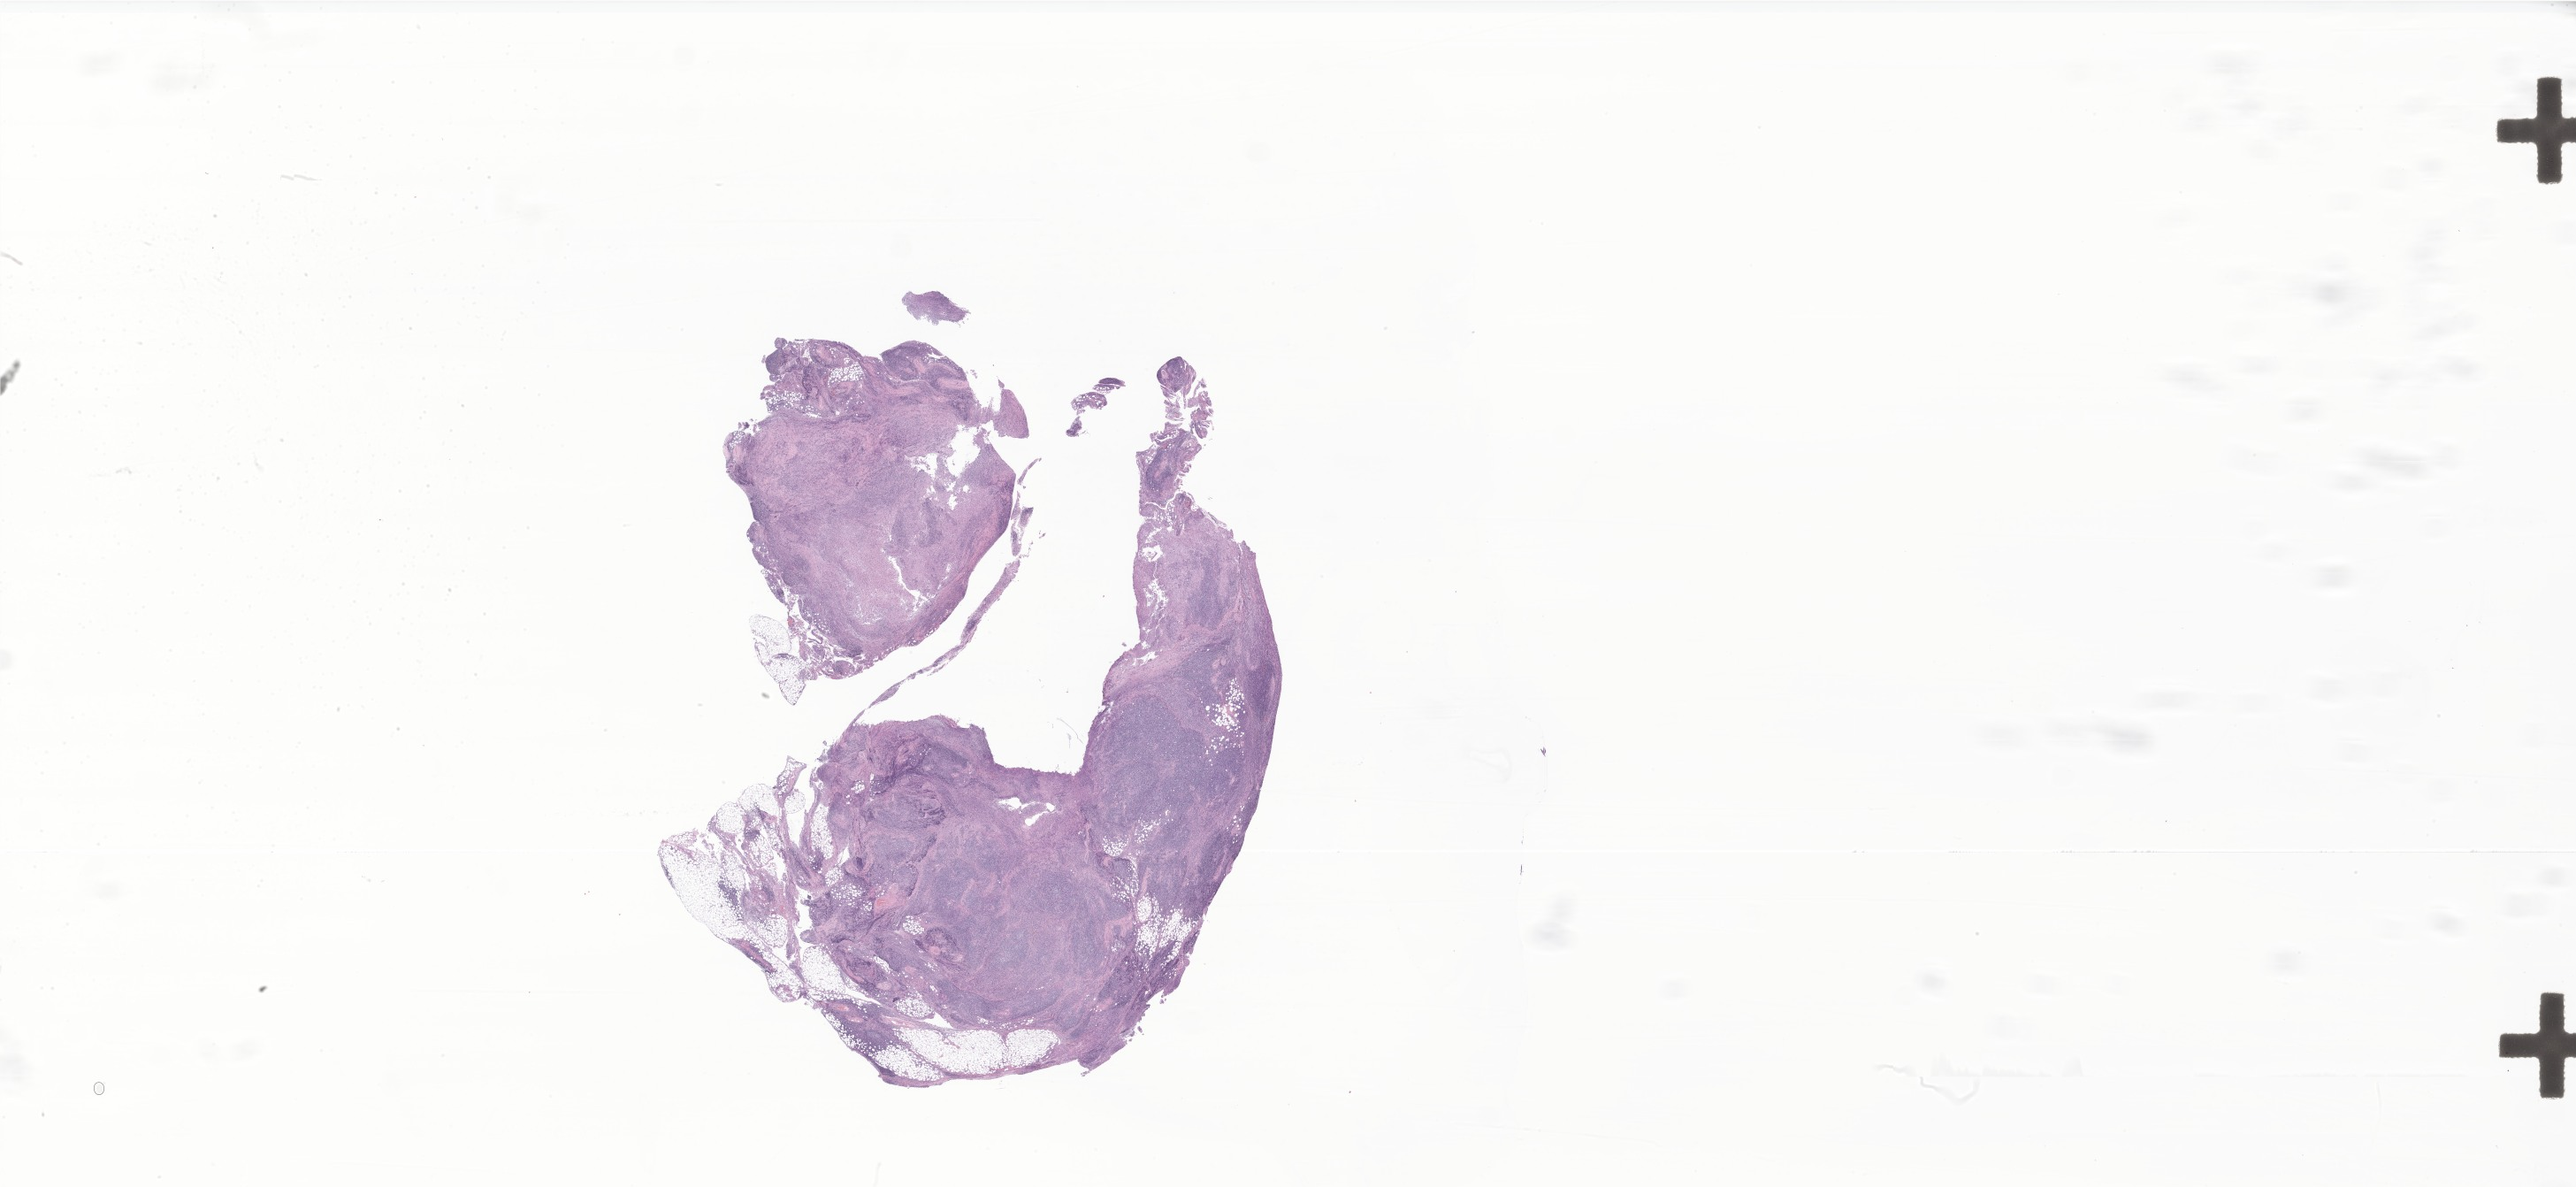
Haematoxylin and eosin whole-slide image of tumor tissue from the pelvis, whole scanned area (about 49.1 x 22.6 mm) shown as a low-resolution overview. Formalin-fixed, paraffin-embedded (FFPE) tissue. Patient: female, age 173 months (14 years 5 months).
Diagnosis (ICD-O-3 morphology term): Angiomatoid fibrous histiocytoma.